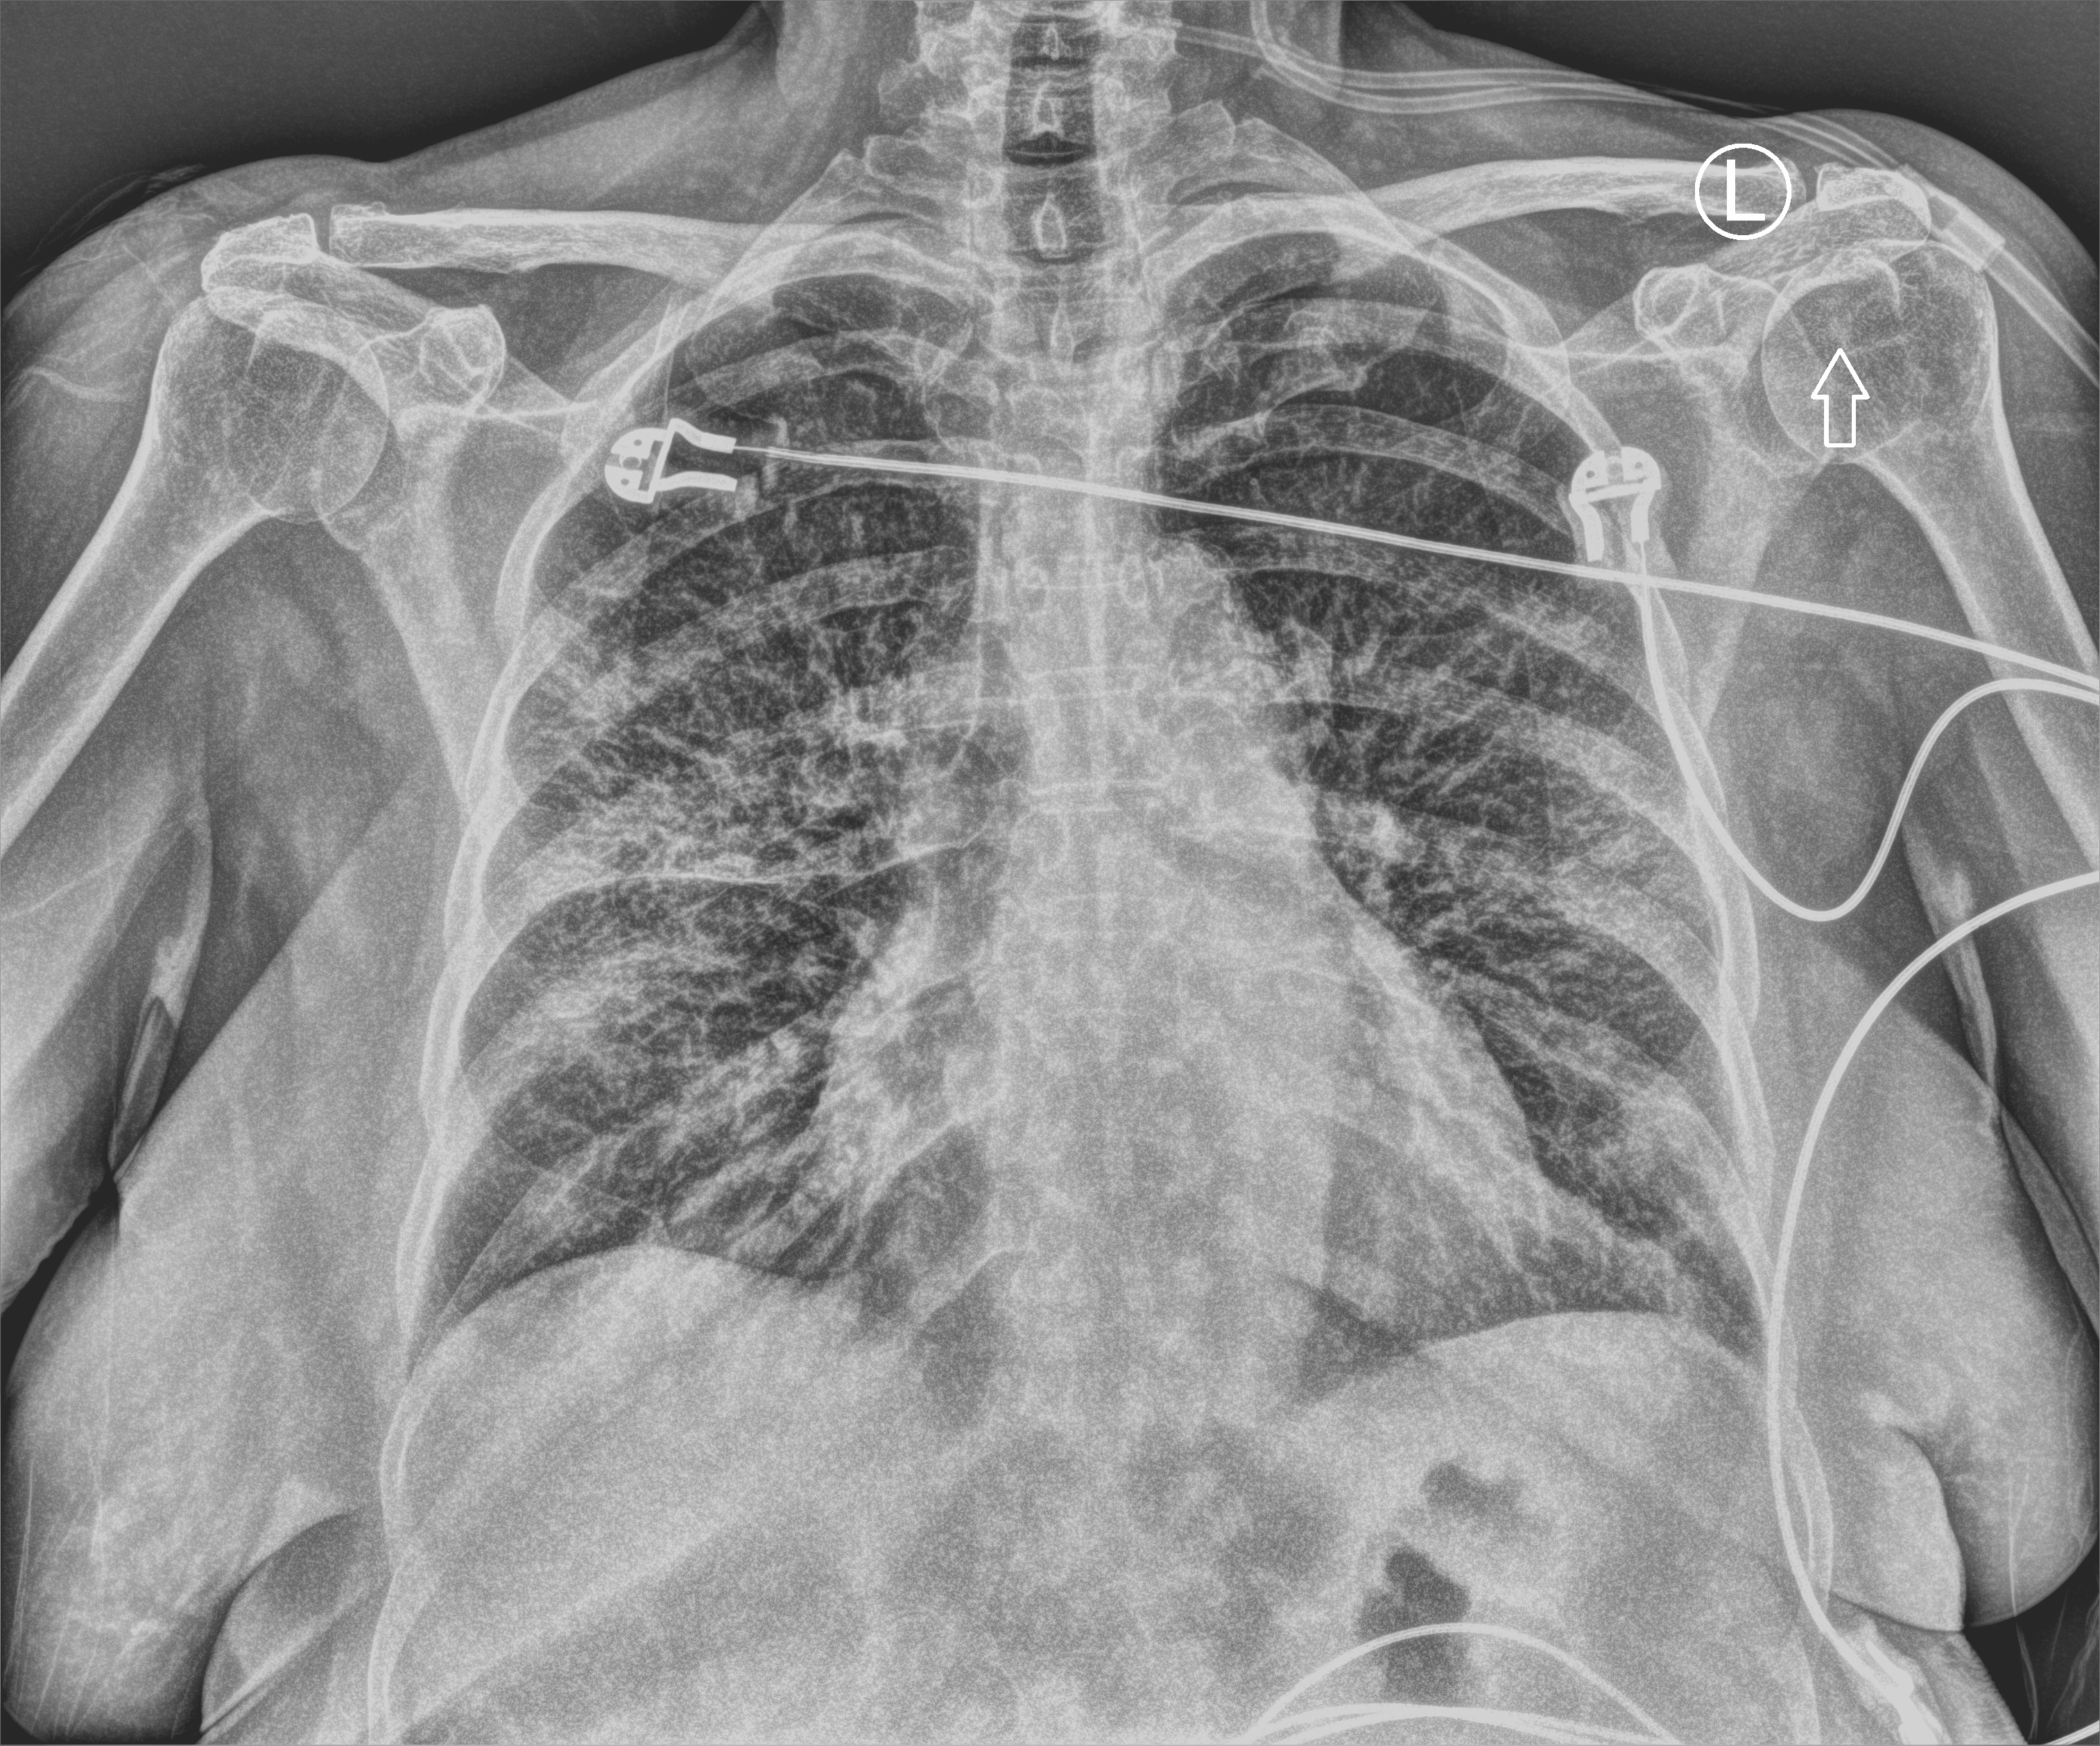
Bedside chest radiograph (computed radiography). Patient hospitalised with COVID-19; female, aged 60–74 years.
Admission-level facts for this patient (not findings on this image; timing relative to this image not recorded): smoking status (admission record): former; admitted to intensive care during this hospital stay: yes; mechanically ventilated during this hospital stay: yes.